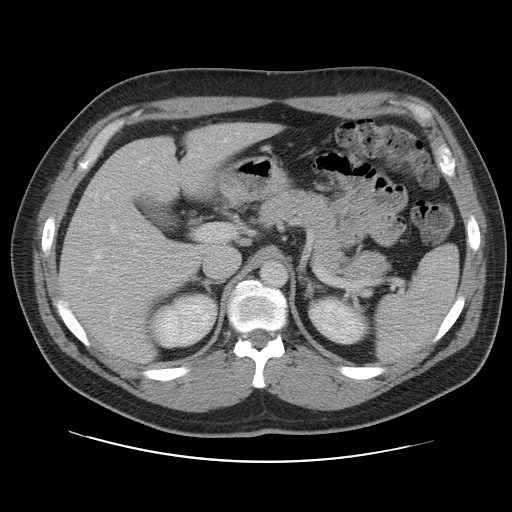
Contrast-enhanced abdominal CT, one axial slice. 120 kVp. Intravenous contrast given. Soft-tissue window (W 400 / L 40 HU). 5 mm slice thickness. 512 × 512 image matrix. Male patient, age 35 years. From the clinical record (not read from this slice): diagnosis: colorectal cancer liver metastases, imaged before liver resection; multiple liver metastases: yes; largest metastasis: 2.8 cm; chemotherapy before resection: yes.
Outlined on this slice (outlined manually by an expert reader):
- hepatic veins: bounding box (x1, y1, x2, y2) in pixels: (86, 138, 228, 313)
- liver: (59, 125, 274, 362)
- planned liver remnant (the part of the liver to remain after resection): (59, 125, 274, 362)
- portal vein (with intrahepatic branches): (87, 225, 208, 286)